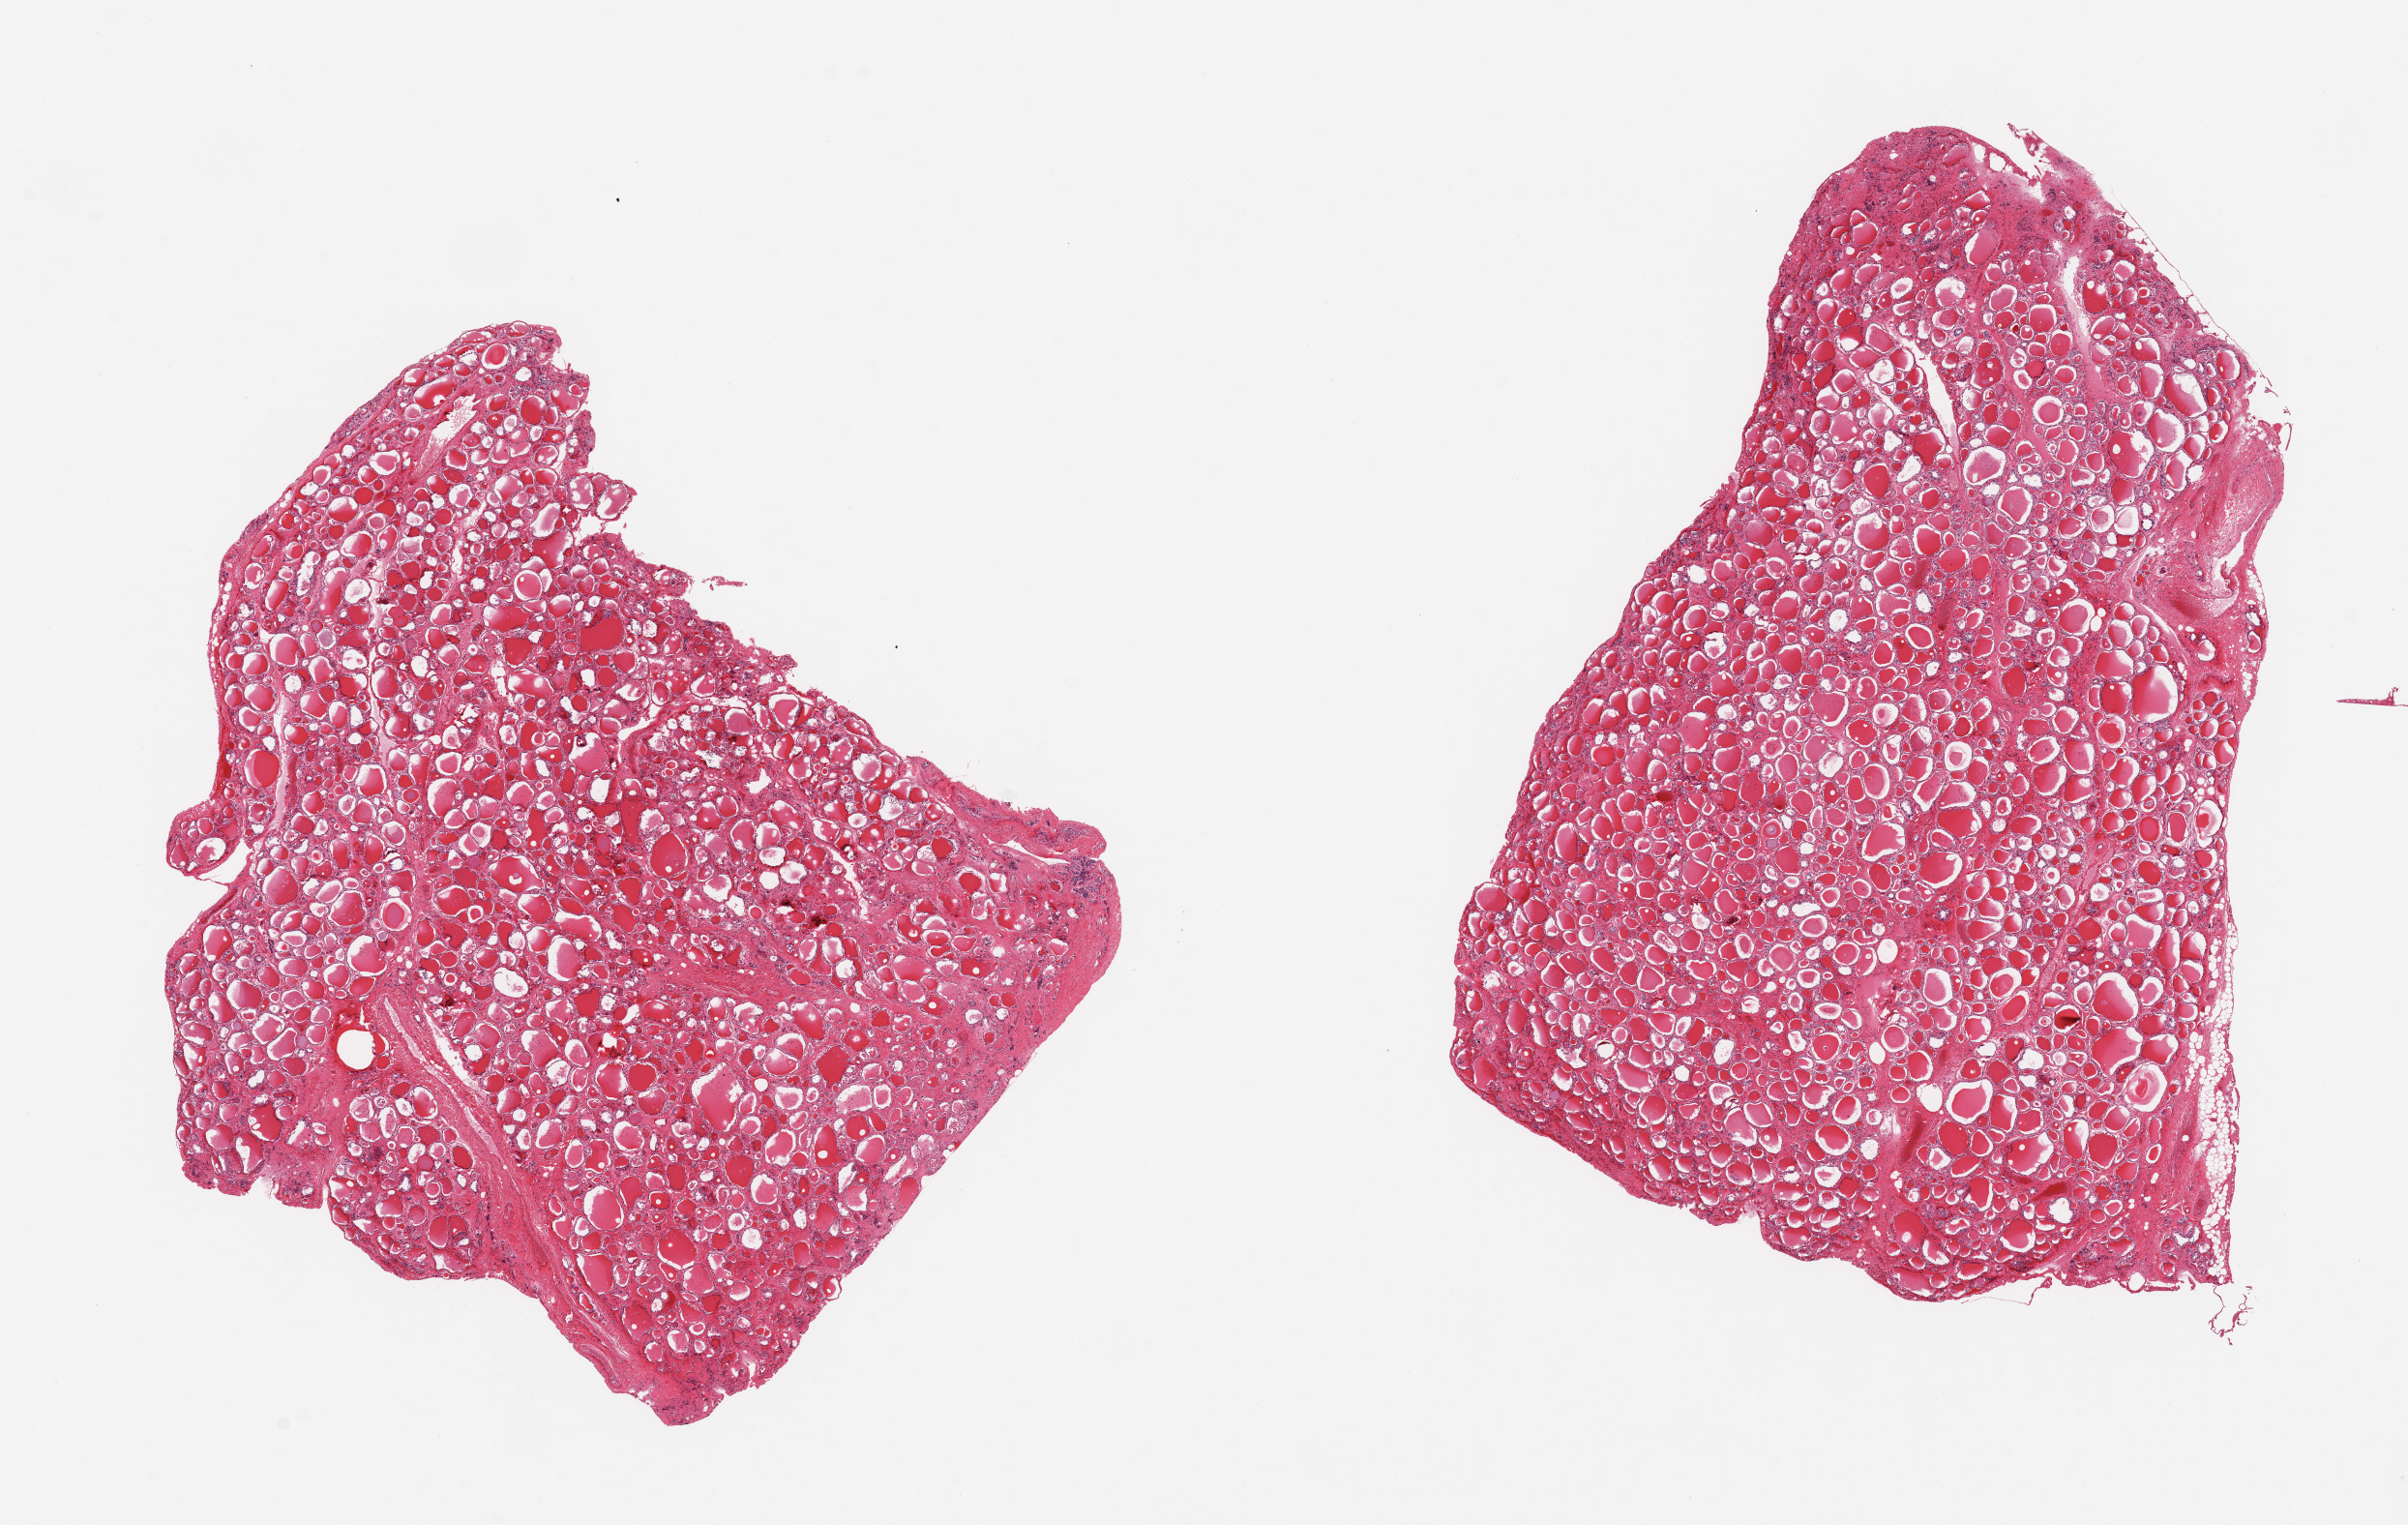
Hematoxylin and eosin (H&E) whole-slide image, shown as a low-resolution overview of the whole scanned area (about 19.7 x 12.5 mm); PAXgene-fixed paraffin-embedded (PFPE) section; target tissue: thyroid; donor tissue sample. Donor sex: female.
• reviewer comment on this tissue sample: 2 pieces, no abnormalities